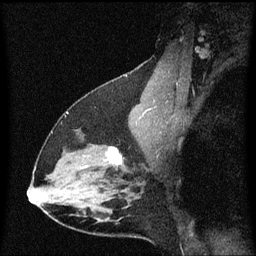
Breast MRI (dynamic contrast-enhanced), one sagittal slice; slice 39 of 60 in the series (ordered by position); dynamic contrast-enhanced series, image 2 of 3 at this slice position (ordered by acquisition); 1.5 T; TE 4.2 ms, TR 8.4 ms; 2 mm slice thickness; 256 × 256 image matrix, field of view 200 × 200 mm. Patient: female, 38 years. Case-level facts recorded for this patient, not image findings: setting: breast cancer imaged before/during neoadjuvant chemotherapy; receptor status: HR-positive, HER2-negative.
Outlined on this slice (semi-automatic segmentation, software-assisted and operator-edited):
- analysis volume of interest (the breast-tissue region the enhancement analysis was run in; not a lesion): box from (x=94, y=144) to (x=139, y=185) px
- tumour enhancement mask (voxels above the 70 % enhancement threshold inside the analysis volume of interest): (x=108, y=148)–(x=123, y=165)